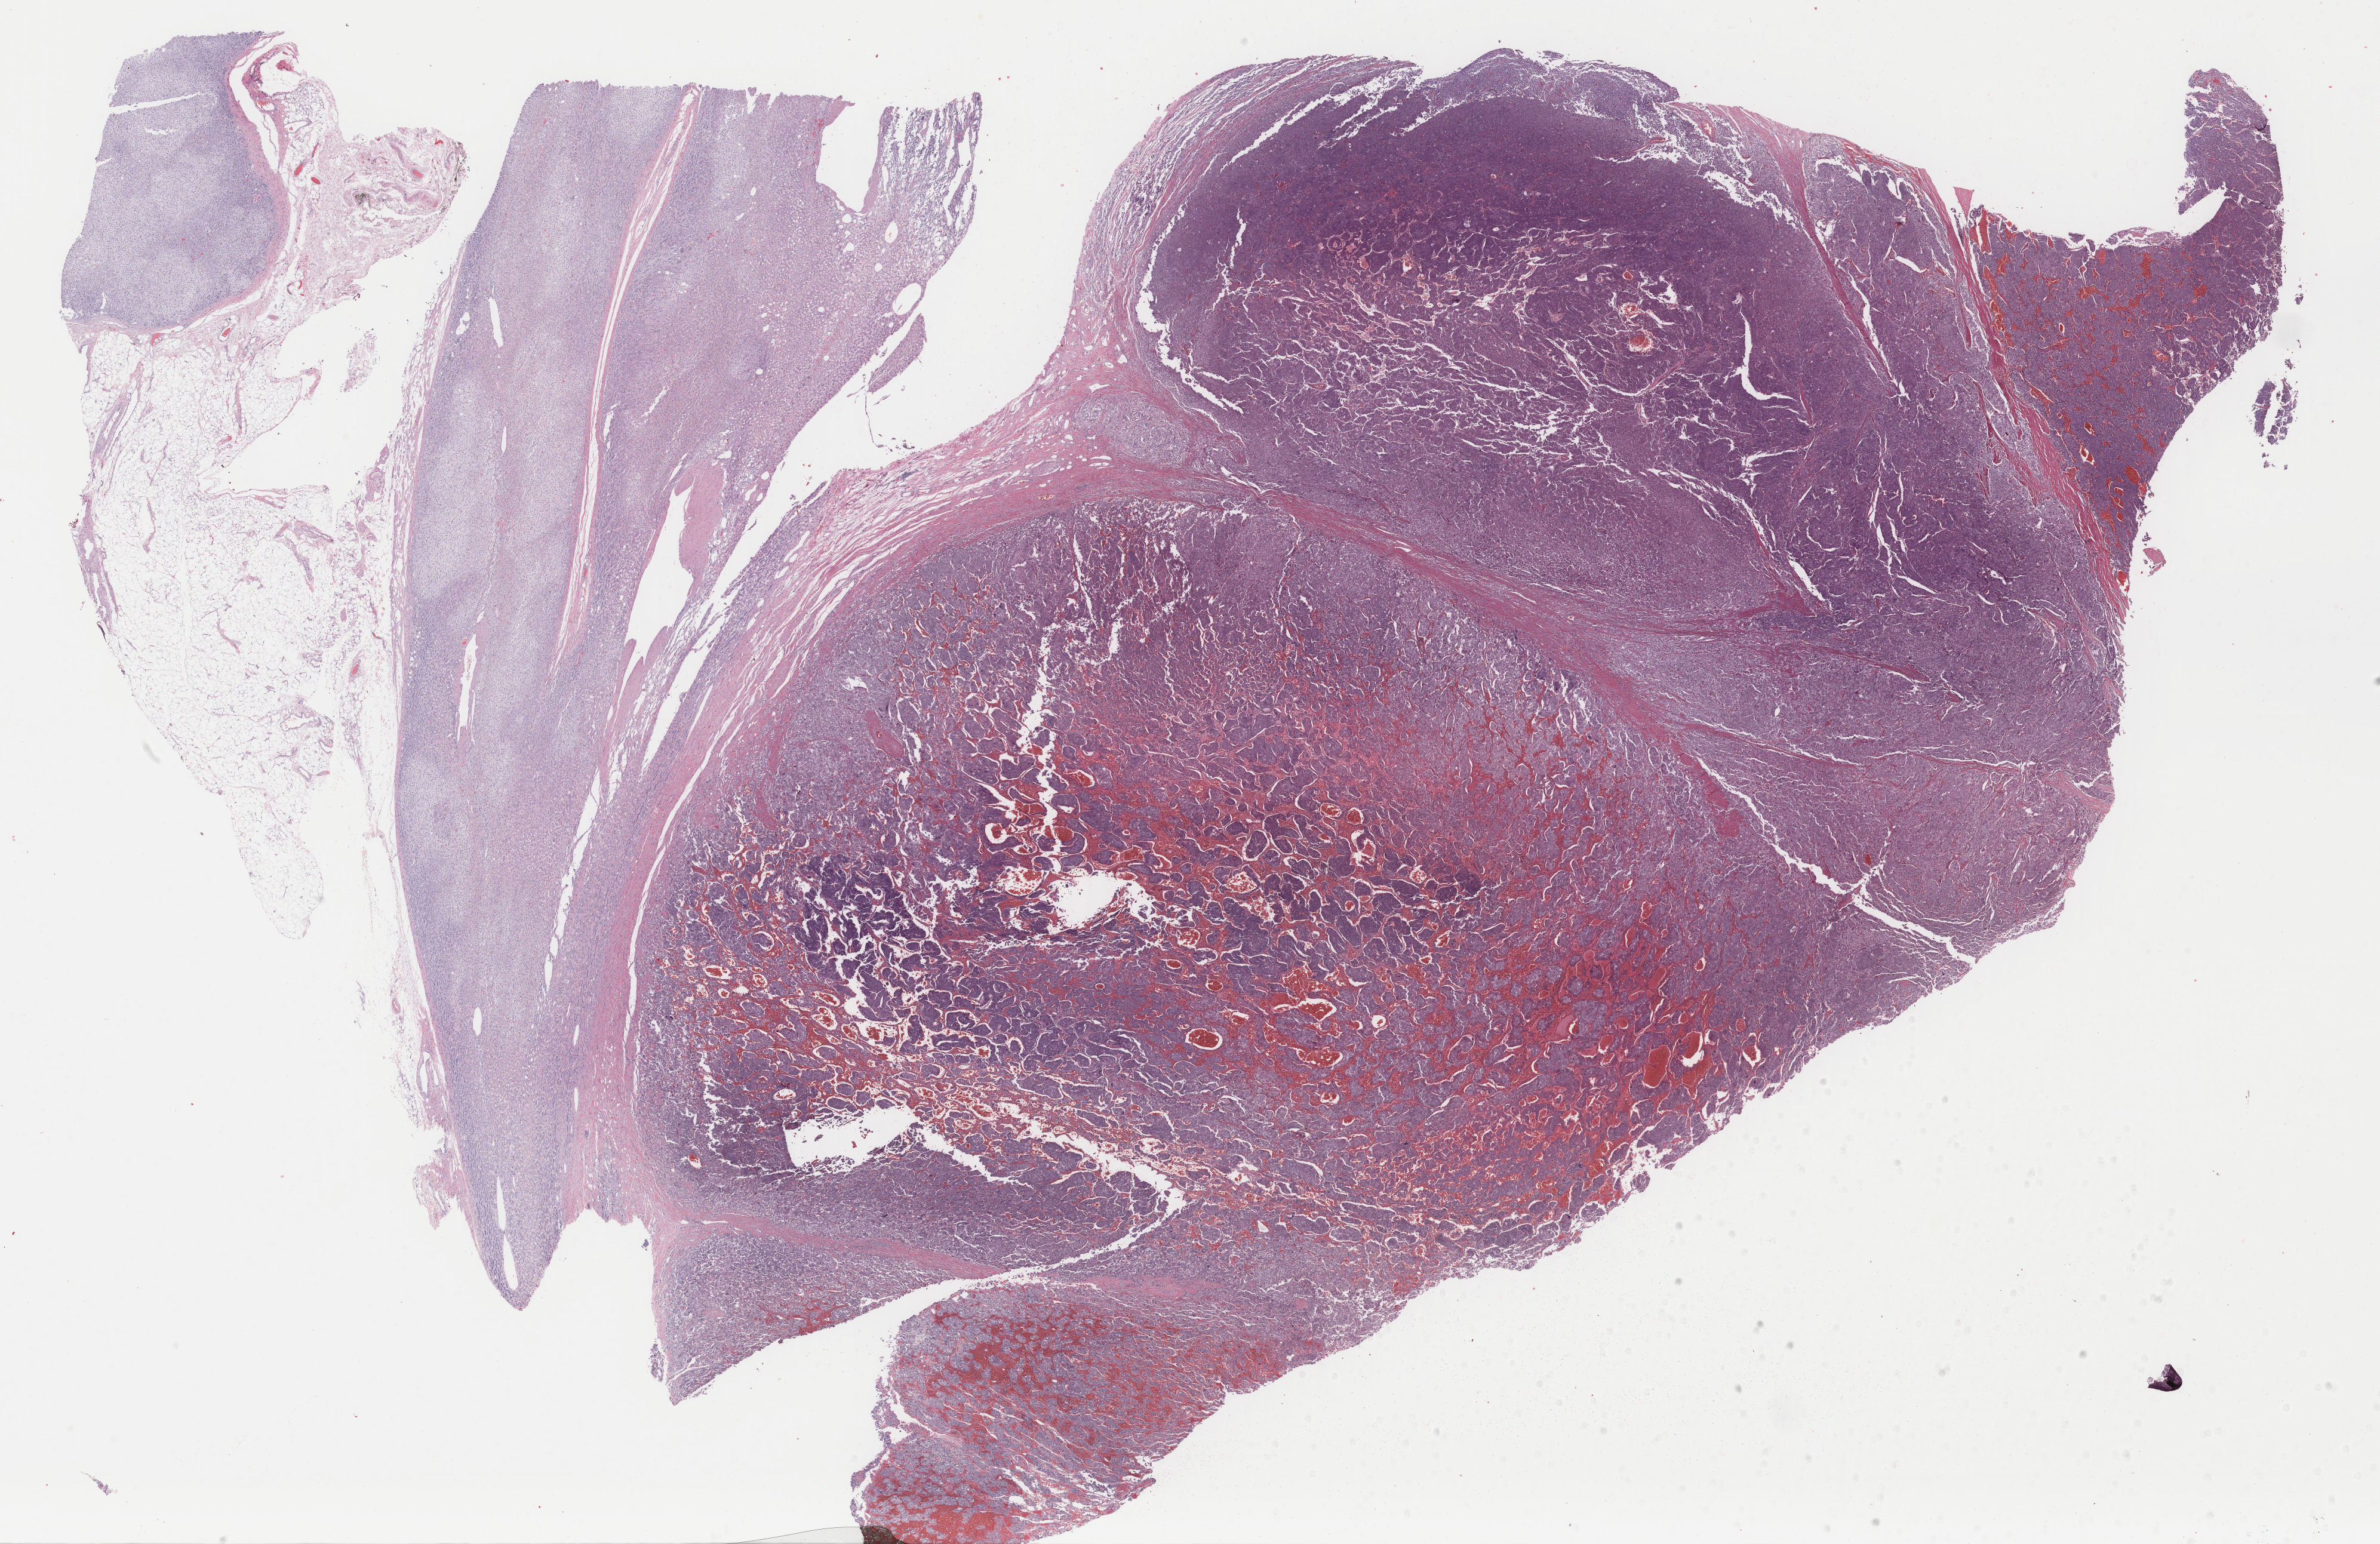
Digitized Hematoxylin and eosin (H&E) stained tissue section (whole slide) — a low-resolution overview of the entire scanned area, about 31.6 x 20.5 mm. Formalin-fixed paraffin-embedded (FFPE) diagnostic section. Adrenal gland, primary tumour sample. Patient: female, age at initial diagnosis 42 years.
Histologic diagnosis: Pheochromocytoma, malignant.